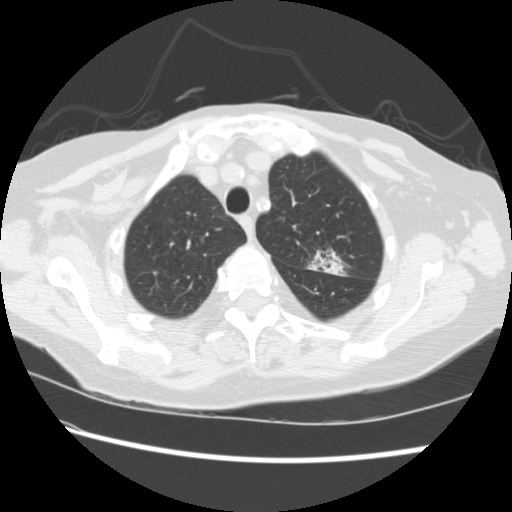
Chest CT (low-dose screening protocol), one axial image; baseline screening round; lung window (W 1500 / L -600 HU); 2.5 mm slice thickness; standard (soft-tissue) reconstruction kernel (STANDARD). Female participant, aged 74 years at enrolment.
Expert-annotated lung lesion, box from (x=297, y=242) to (x=347, y=282) px. The screening reader recorded 2 non-calcified nodules or masses ≥4 mm on this exam (left upper lobe, right lower lobe); which of them this box marks is not recorded.